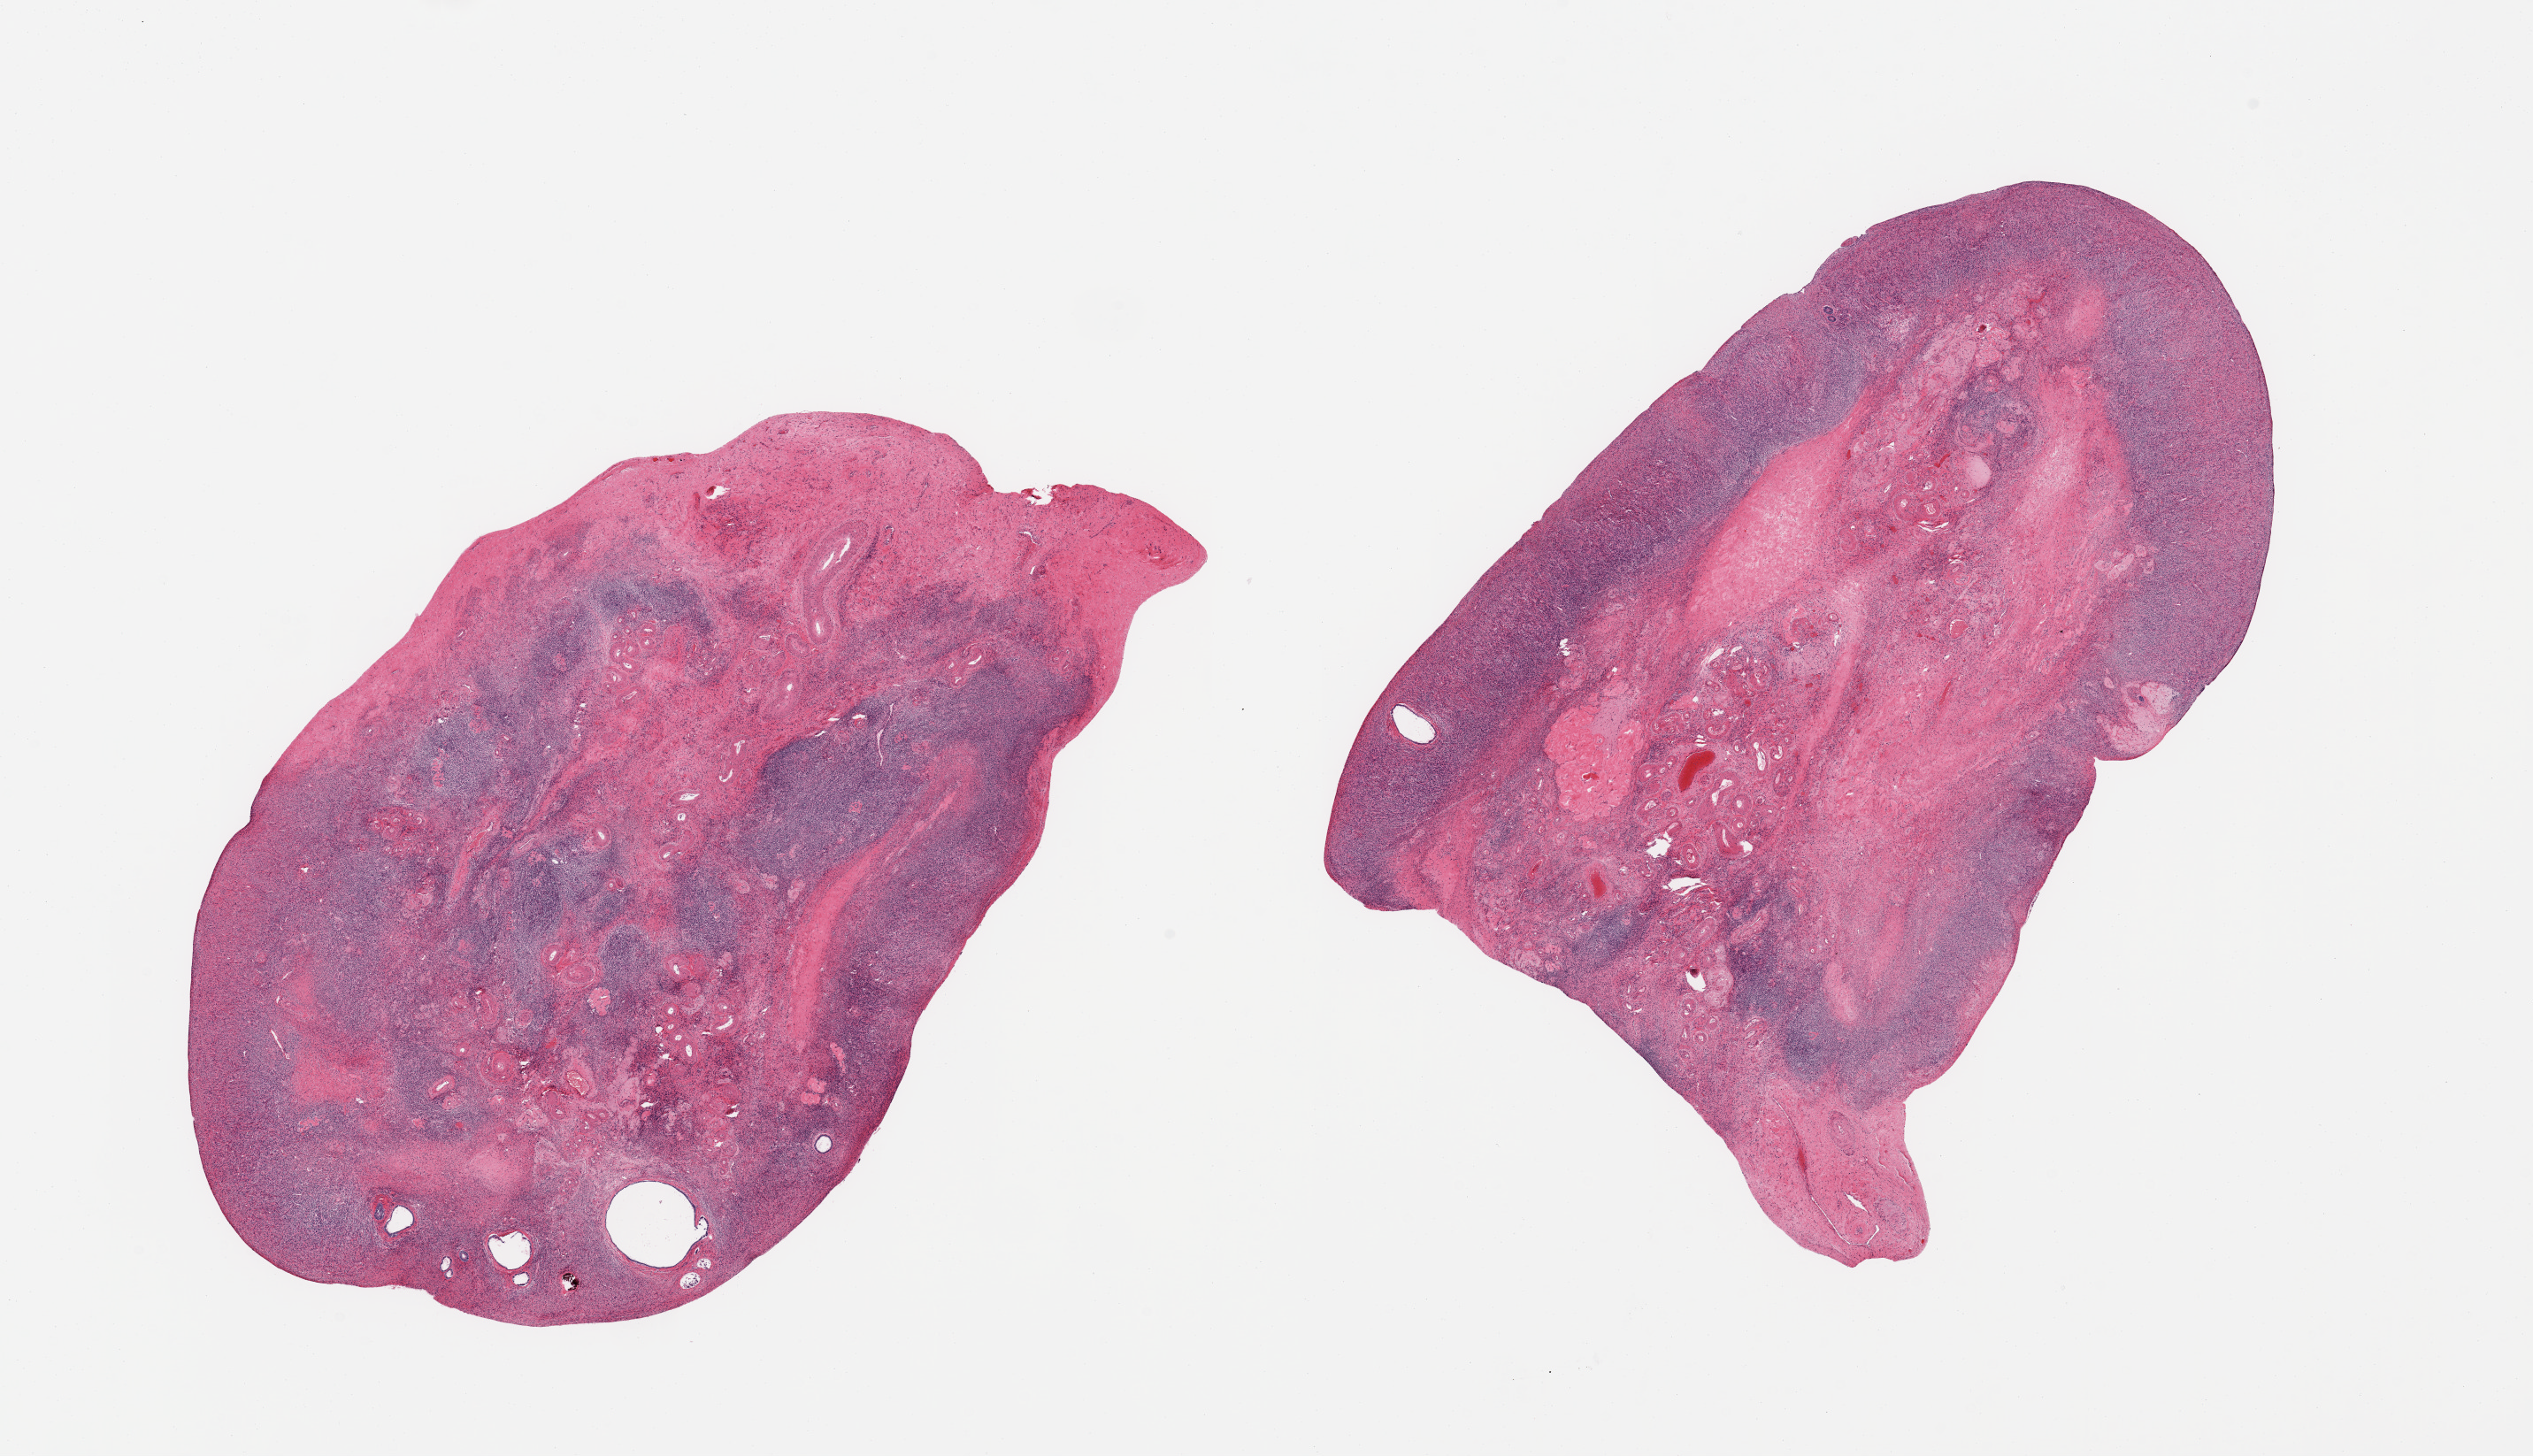
Digitized hematoxylin and eosin (H&E)-stained section — a low-resolution overview of the entire scanned area, about 22.6 x 13.0 mm, PAXgene-fixed paraffin-embedded (PFPE) section, sampled site (target tissue): ovary, donor tissue sample. Female donor.
Pathologist's review note for this sample: 2 pieces; atrophic; several small simple cysts; small corpora albicantia.